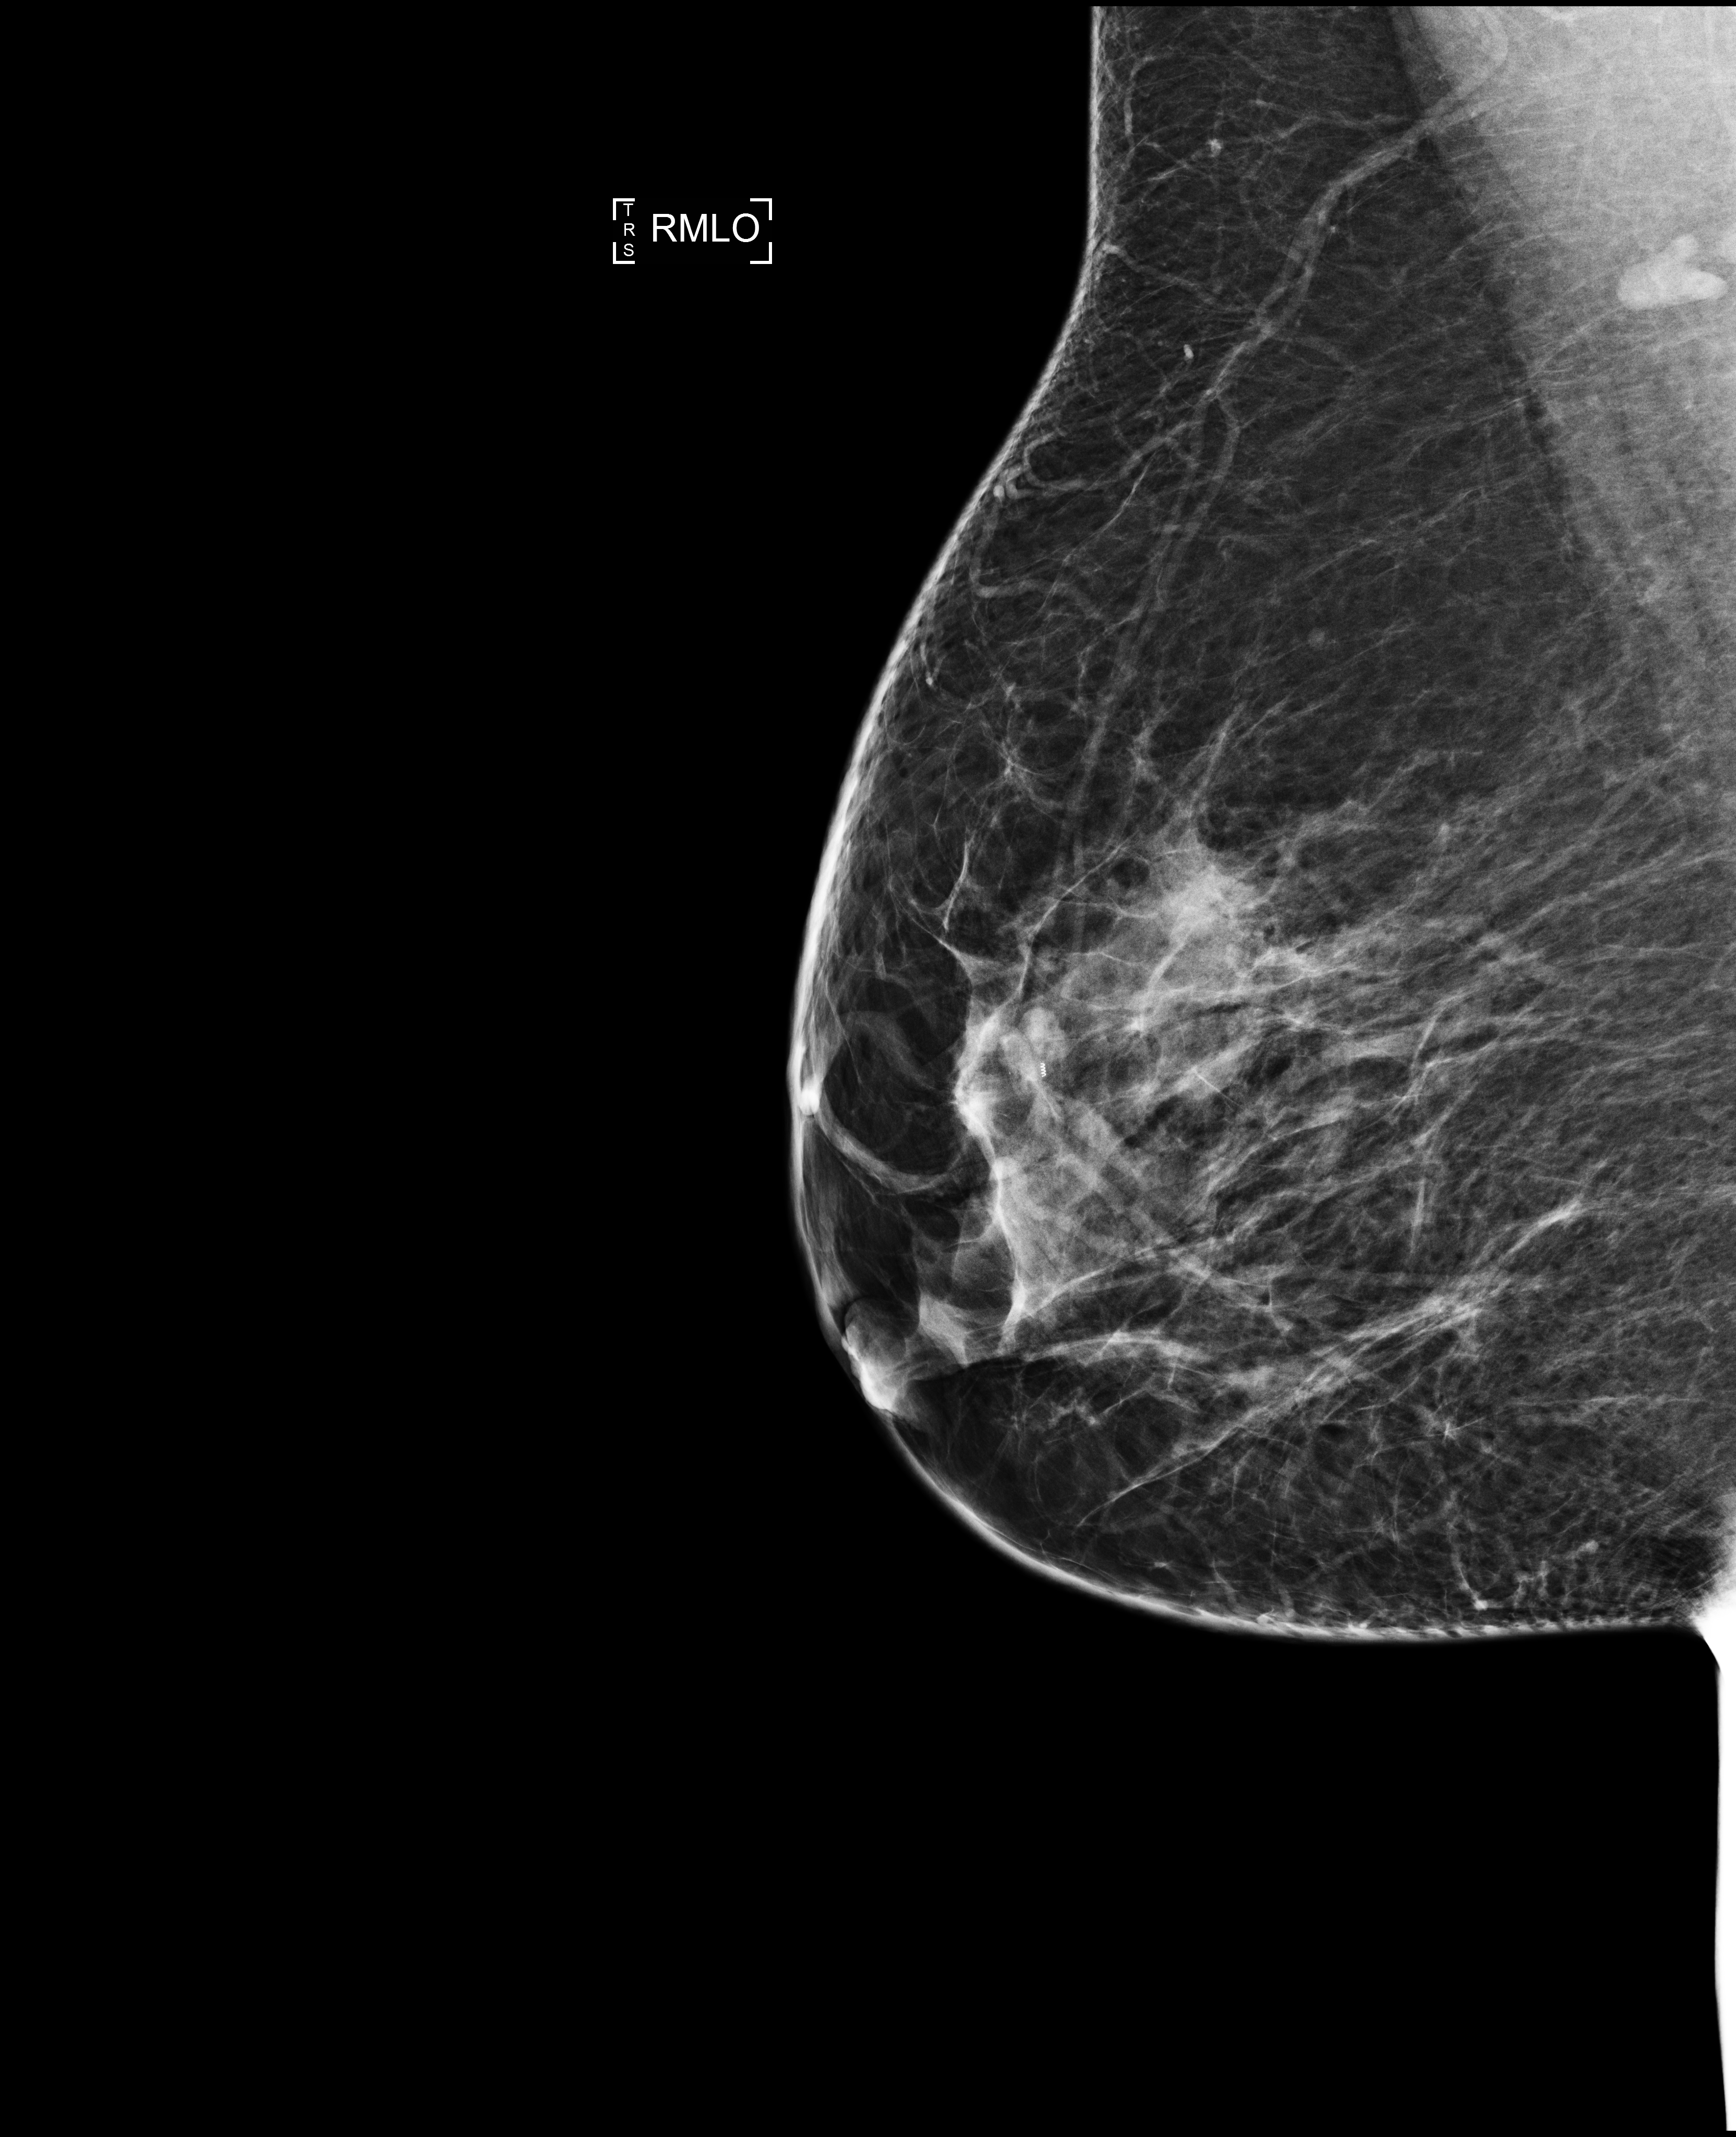
Annual screening mammography examination; compressed breast thickness 63 mm; system: Selenia Dimensions. Patient aged 47 years (female).
Image type: full-field digital mammogram. Breast: right. Projection: mediolateral oblique (MLO) view.